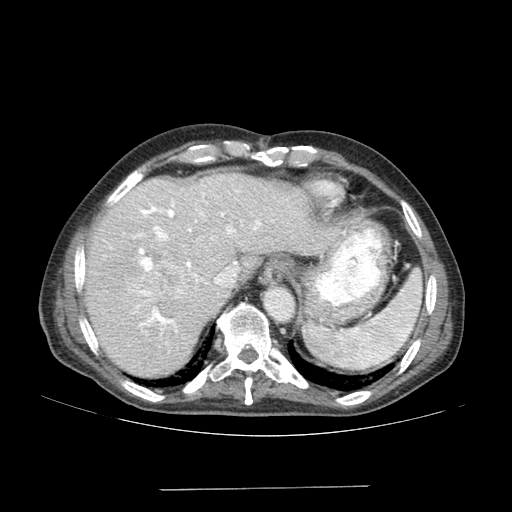
Contrast-enhanced abdominal CT (liver protocol), one axial slice. Reconstruction kernel SOFT. Soft-tissue window (W 400 / L 40 HU). 2.5 mm slice thickness. 512 × 512 image matrix. From the clinical record (not read from this slice): diagnosis: hepatocellular carcinoma (patient treated with transarterial chemoembolisation; whether this scan precedes or follows treatment is not stated here); TNM stage (as recorded): Stage-IVA; Child-Pugh class: A; tumour differentiation: poorly differentiated; tumour nodularity: uninodular.
Structures marked on this image (semi-automatic segmentation, software-assisted and operator-edited):
- liver parenchyma outside the tumour (the mass and vessels are separate outlines, so this box may not span the whole liver): box from (x=84, y=174) to (x=336, y=376) px
- mass: (x=127, y=262)–(x=190, y=302)
- liver vessels: (x=115, y=192)–(x=261, y=332)